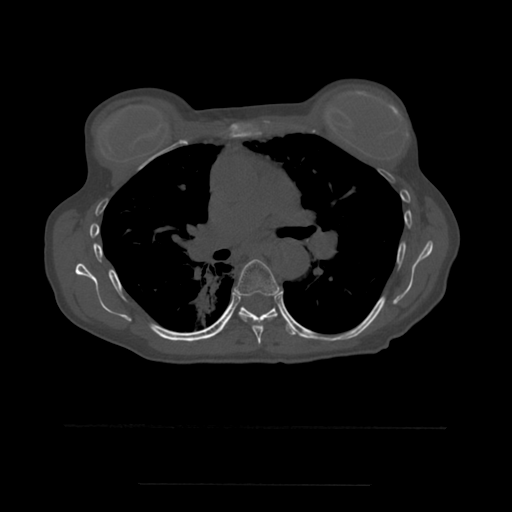
CT including the spine, one axial slice; slice 368 of 544 in the series (ordered by position); bone window (W 1800 / L 400 HU); 1.25 mm slice thickness; 512 × 512 image matrix. Patient age 58 years. Case-level facts recorded for this patient, not image findings: primary cancer: lung.
Outlined on this slice (semi-automatically segmented with operator editing):
- T6 vertebra: bounding box [x1, y1, x2, y2] px = [234, 259, 280, 345]
- T7 vertebra: [220, 306, 295, 336]